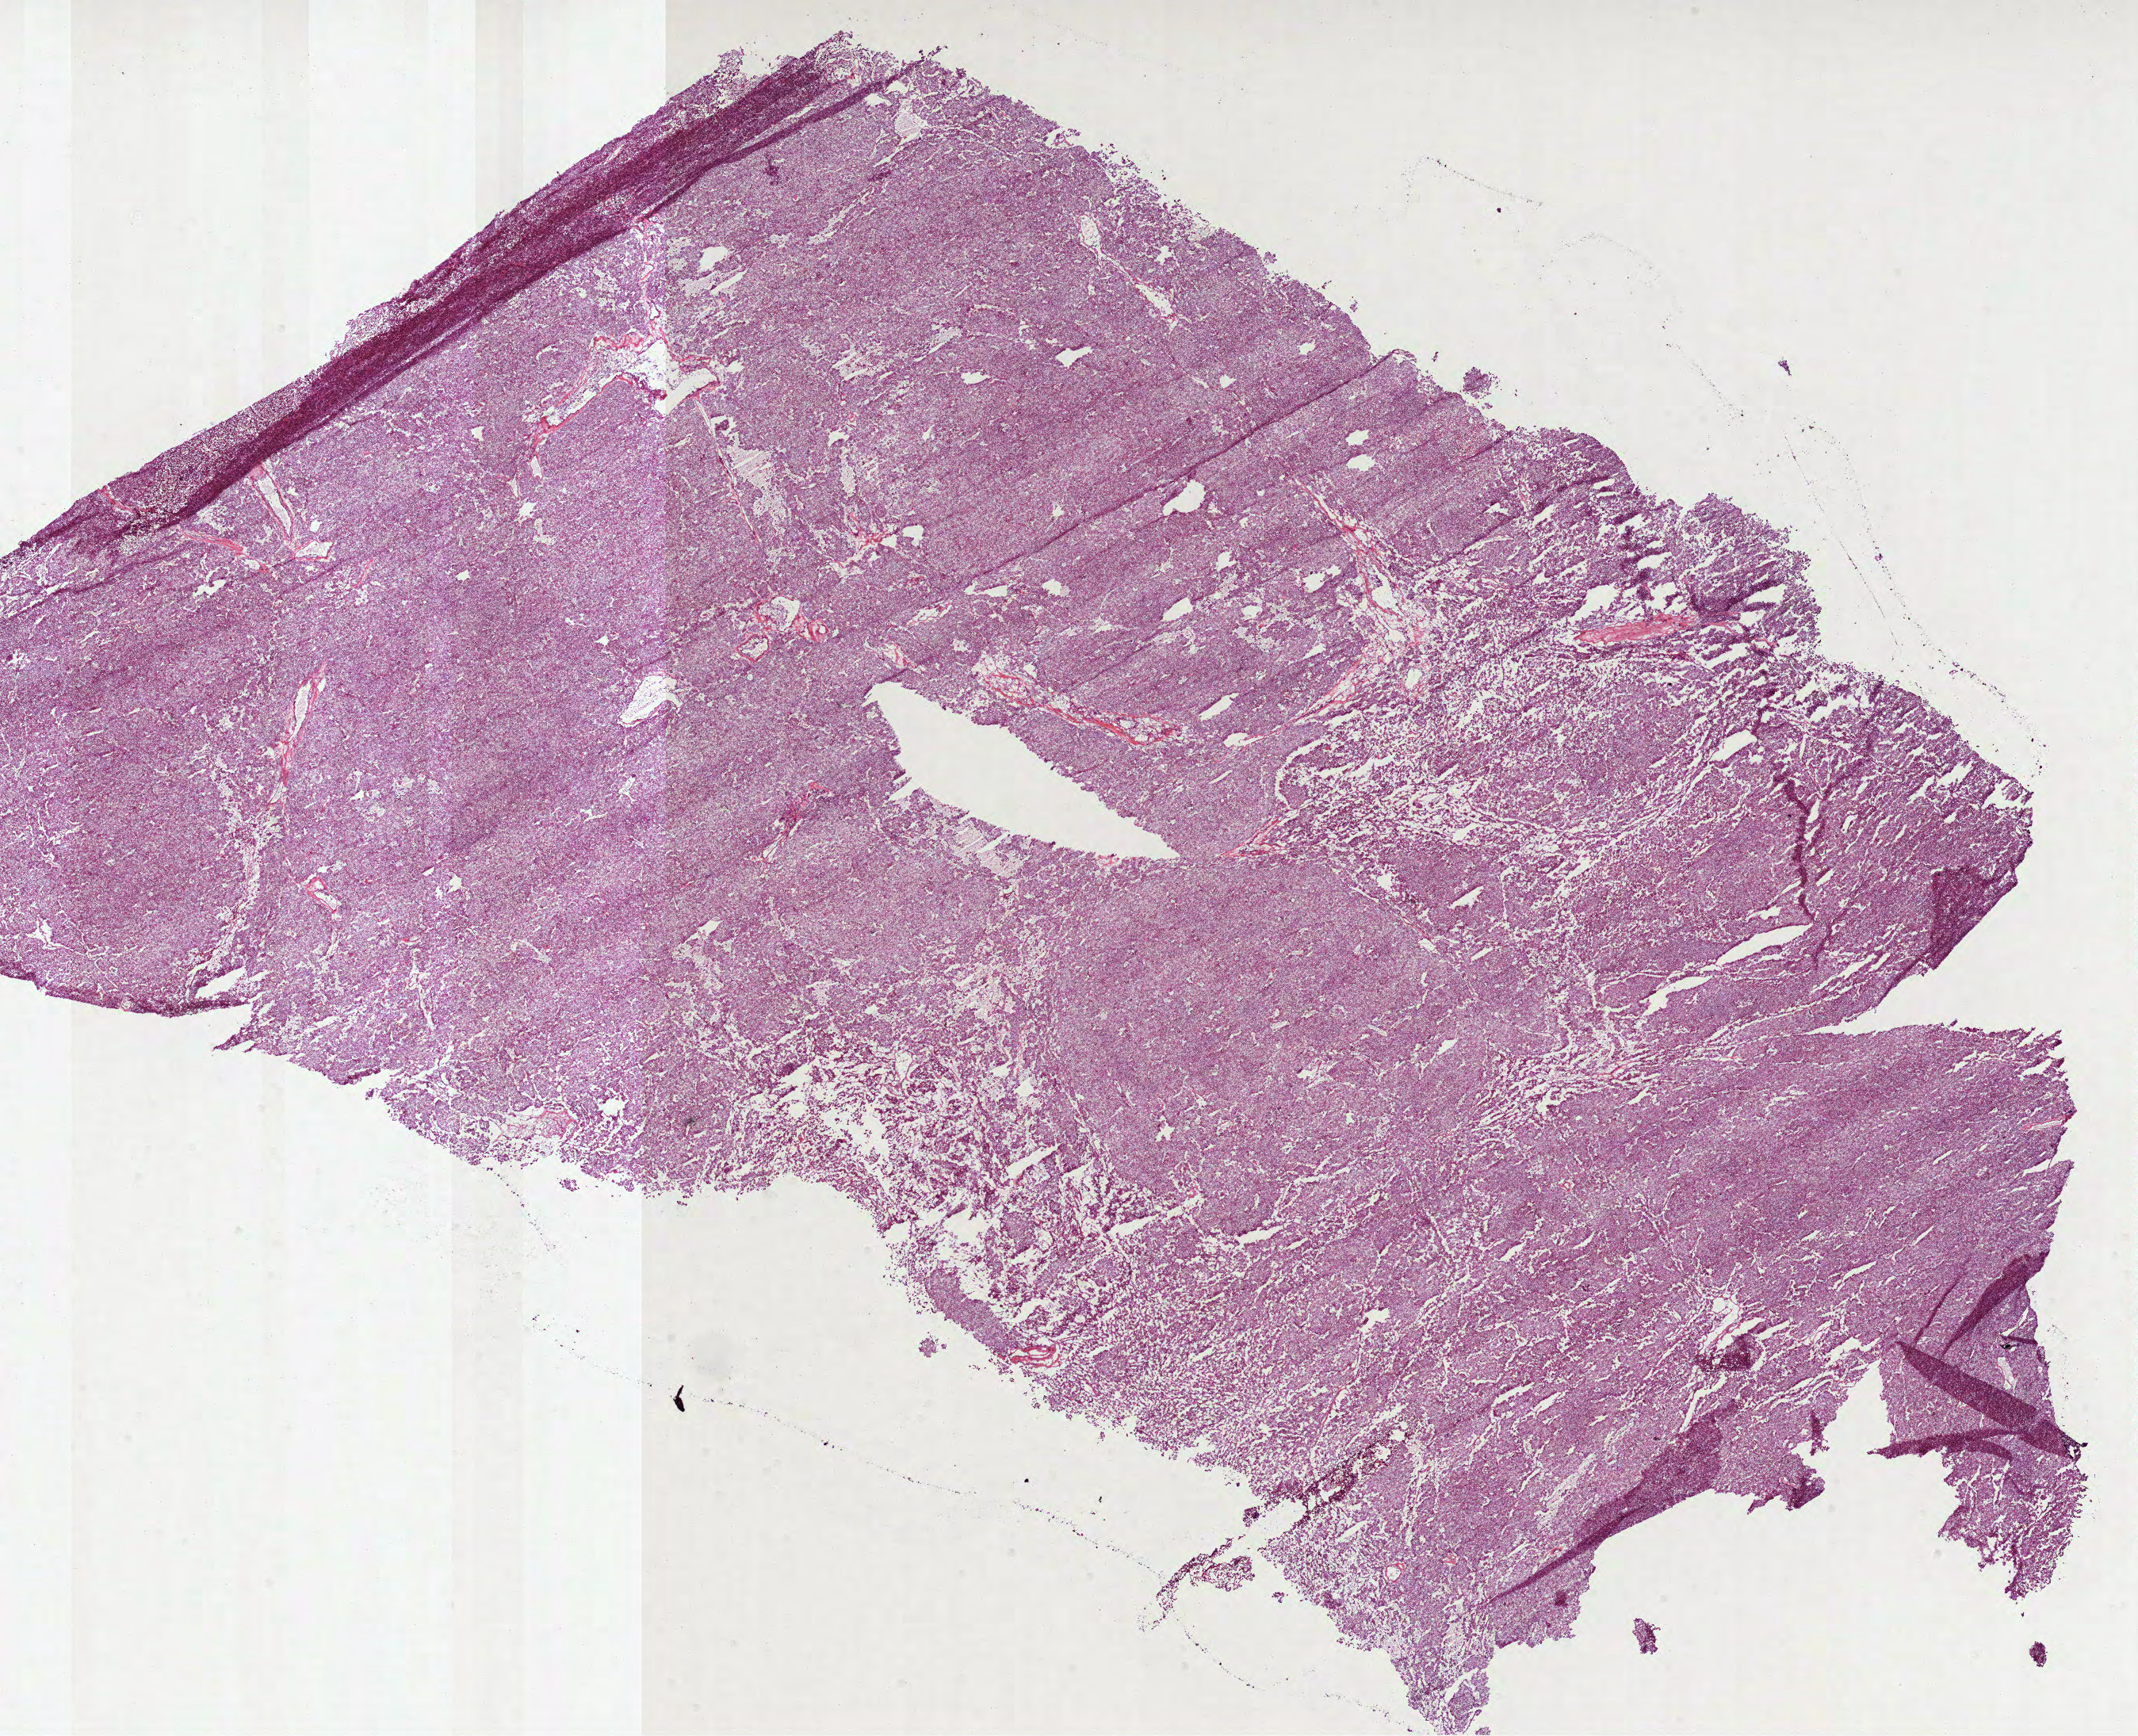
Digitized H&E-stained tissue section (whole slide) — shown as a low-resolution overview of the whole scanned area (about 21.8 x 17.7 mm); frozen section from the bottom of the tissue portion; kidney, primary tumour sample. Patient: male, age at initial diagnosis 43 years. Composition of this section per pathologist review: tumour cells 100%, tumour nuclei 95%, normal cells 0%, stromal cells 0%, necrosis 0%. Infiltration values recorded for this section: lymphocyte infiltration 0%, monocyte infiltration 0%, neutrophil infiltration 0%.
* AJCC pathologic stage: II (6th edition)
* histologic diagnosis: Renal cell carcinoma, chromophobe type